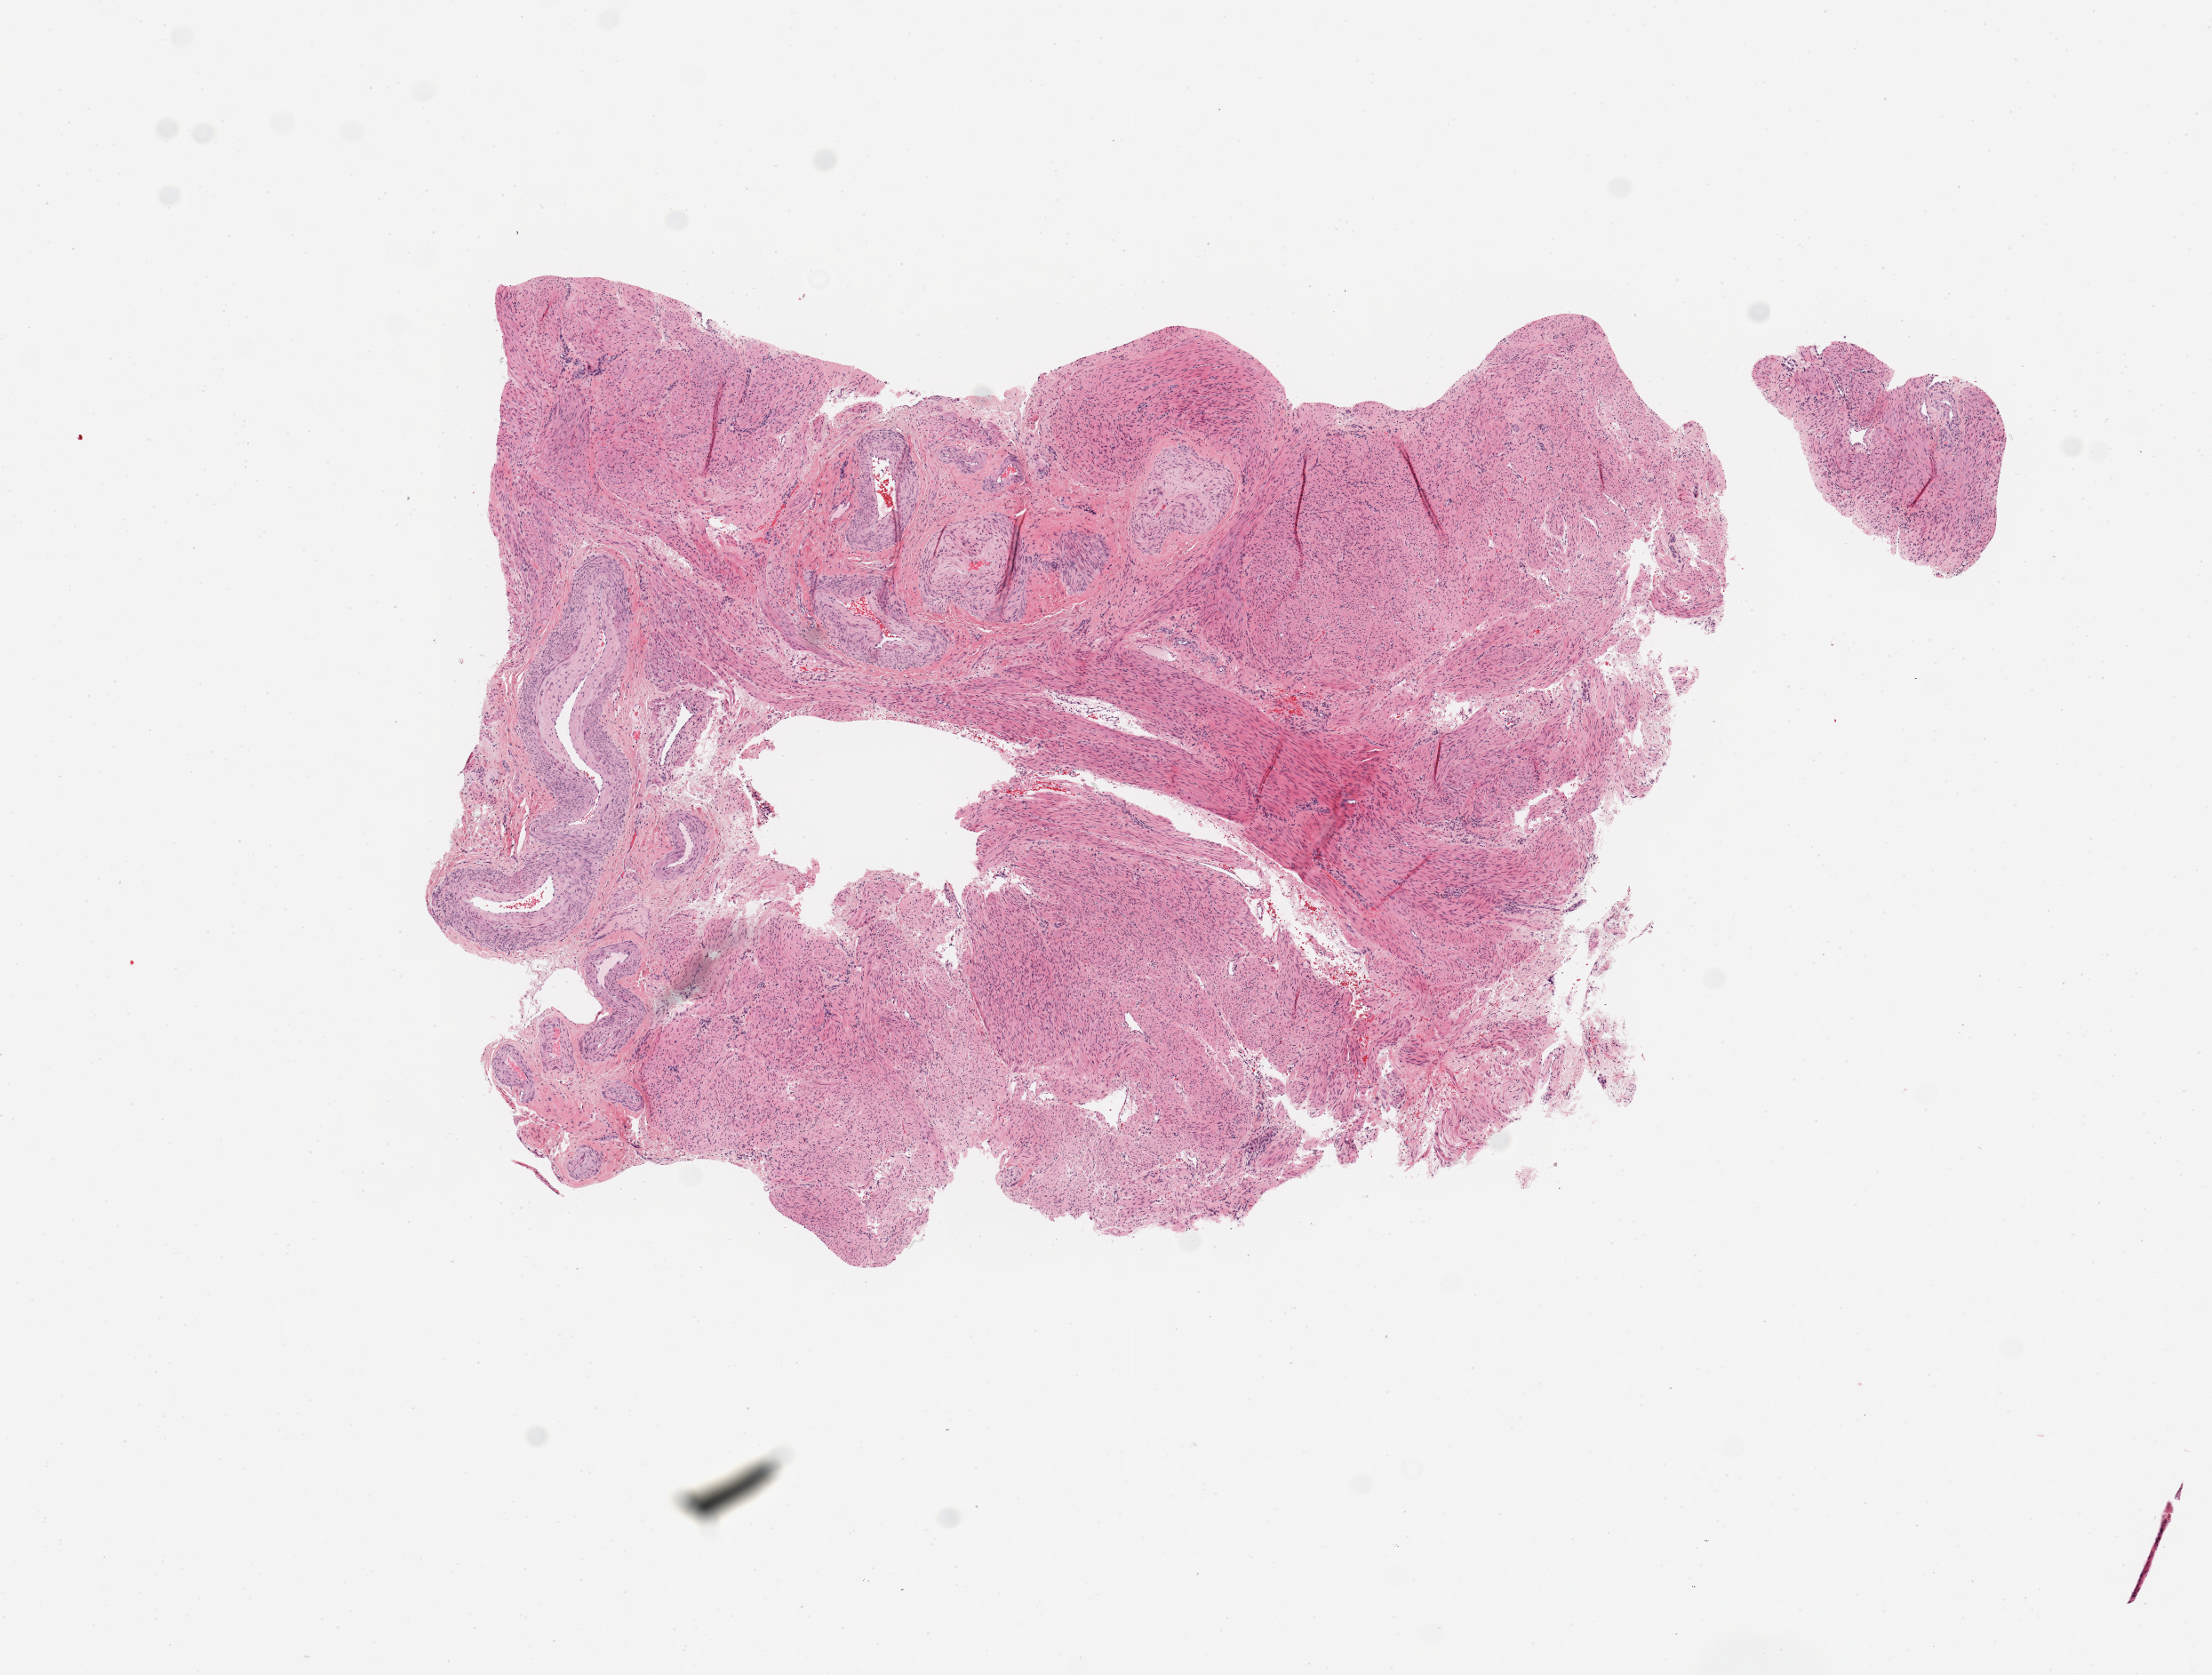
Whole-slide histology image, H&E-stained — a low-resolution overview of the entire scanned area, about 9.8 x 7.5 mm; uterus, normal (non-tumour) tissue. Female, 69 y/o.
This section: normal (non-tumour) tissue from the same patient. Patient diagnosis: Endometrioid adenocarcinoma, NOS.